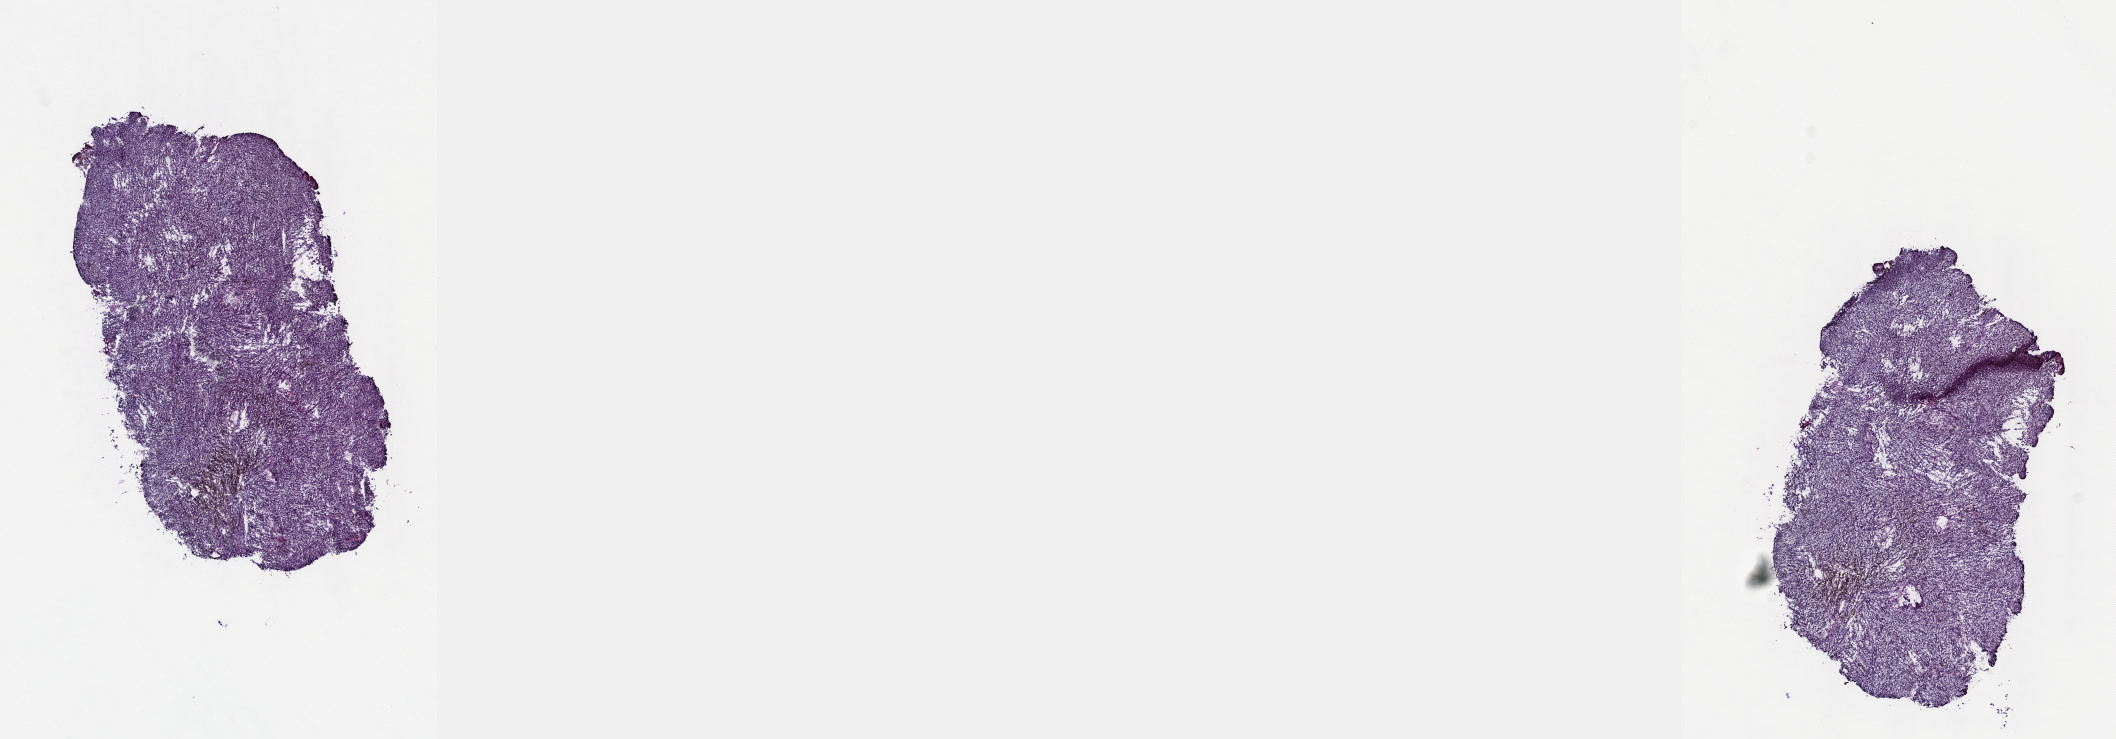
H&E whole-slide image — low-resolution overview of the scanned area, about 17.1 x 6.0 mm; frozen section from the top of the tissue portion; sample: primary tumour, uvea. Male patient; age at initial diagnosis 22 years. Slide review estimates, as recorded: tumour cells 100%, tumour nuclei 80%, normal cells 0%, stromal cells 0%, necrosis 0%. Infiltration values recorded for this section: lymphocyte infiltration 2%, monocyte infiltration 0%, neutrophil infiltration 0%.
Diagnosis: Mixed epithelioid and spindle cell melanoma (choroid). AJCC pathologic stage: IIB (7th edition). Laterality: right.